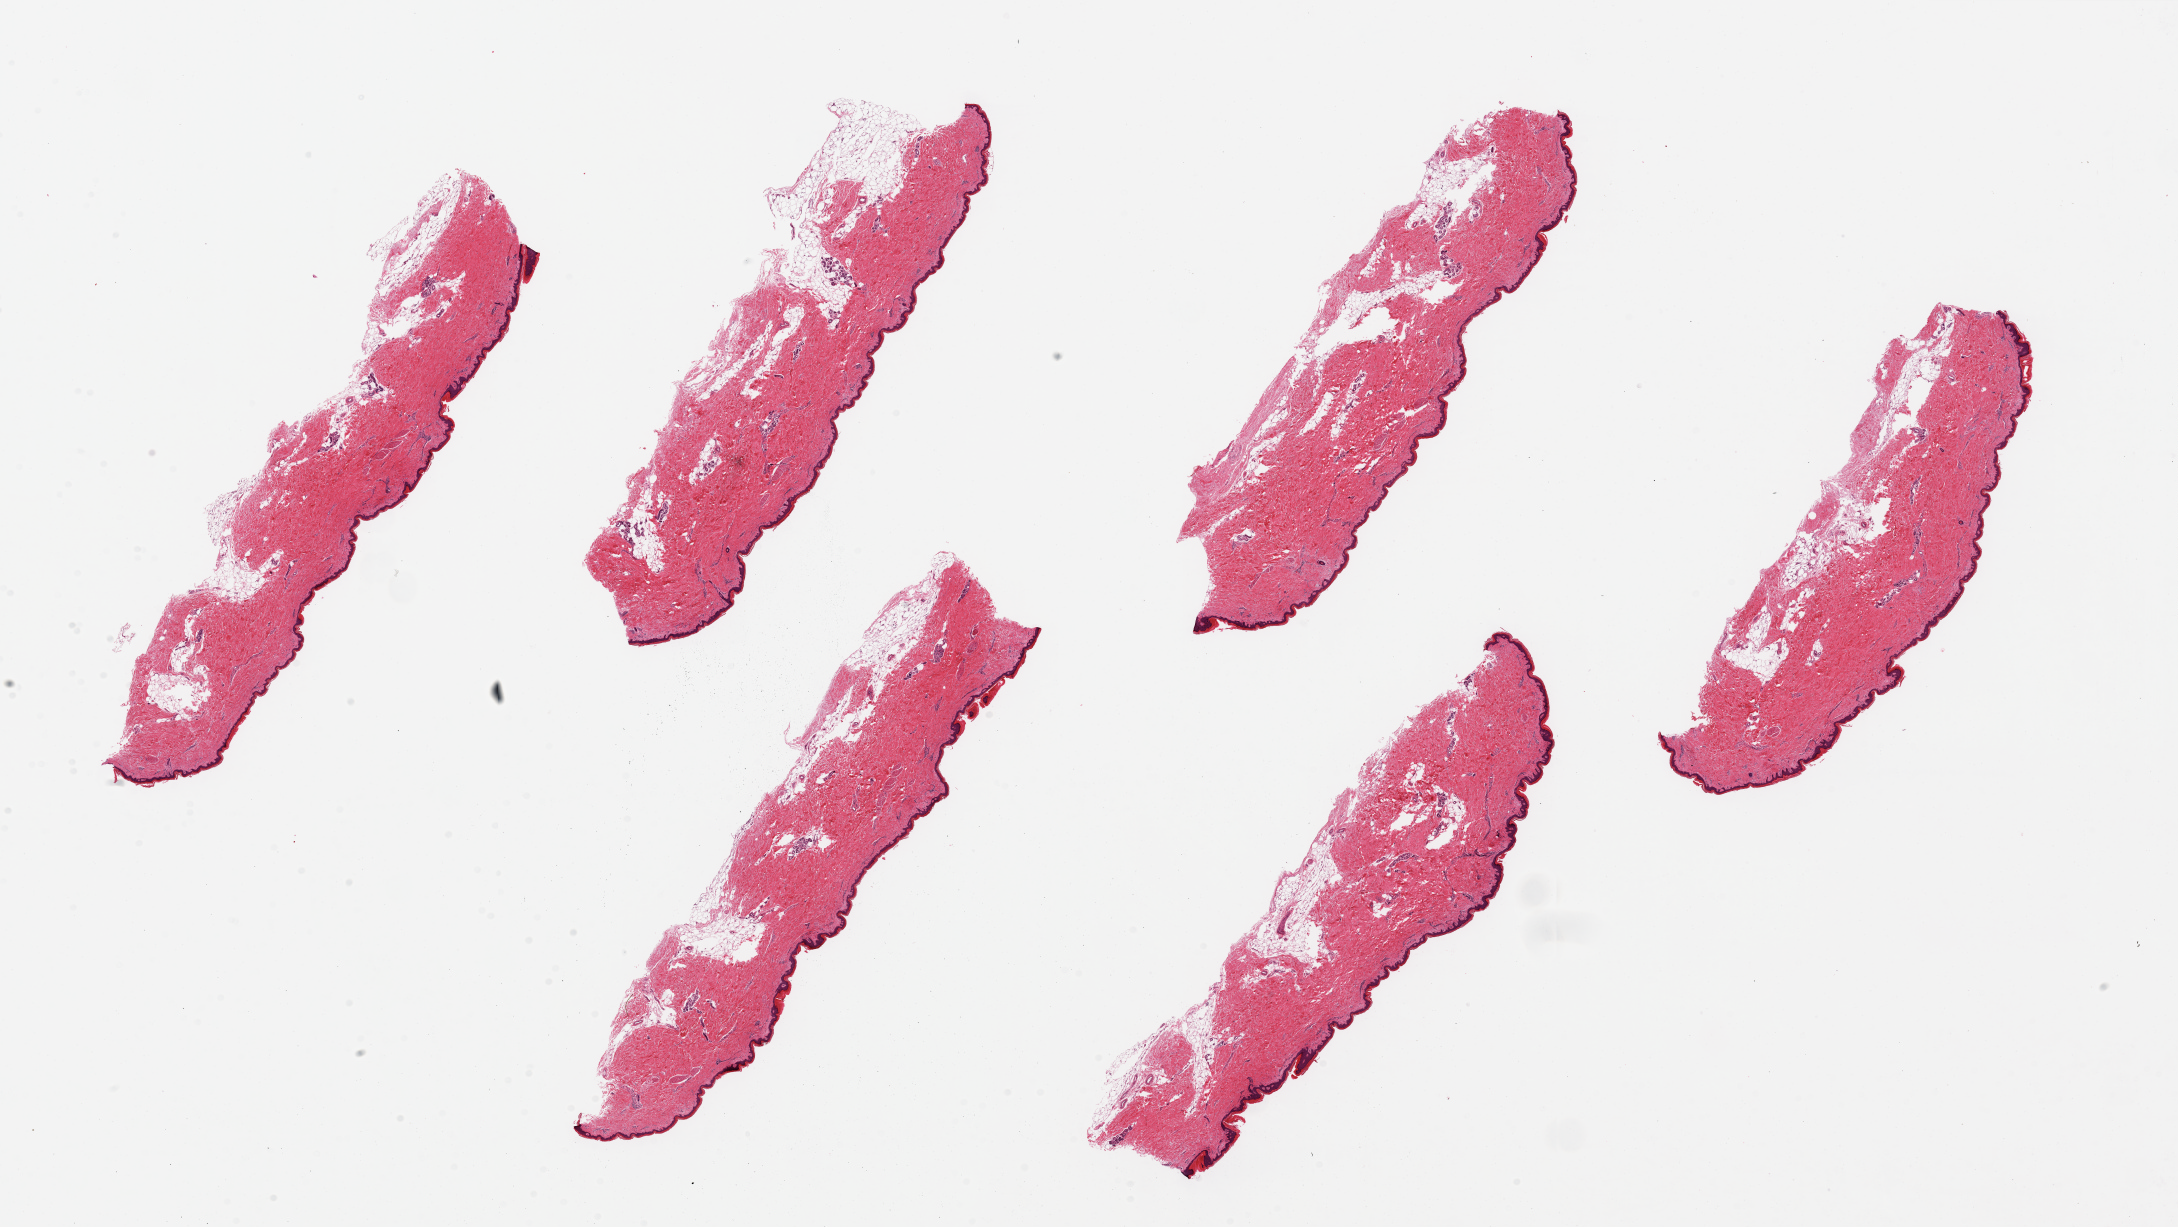
H&E whole-slide image, brightfield — shown as a low-resolution overview of the whole scanned area (about 34.5 x 19.4 mm, from a 20x scan), PAXgene-fixed paraffin-embedded (PFPE) section, target tissue: skin of lower leg, donor tissue sample.
Reviewer comment on this tissue sample: 6 pieces, up to 11x2mm; squamous epitherlium is ~2-3% of thickness.